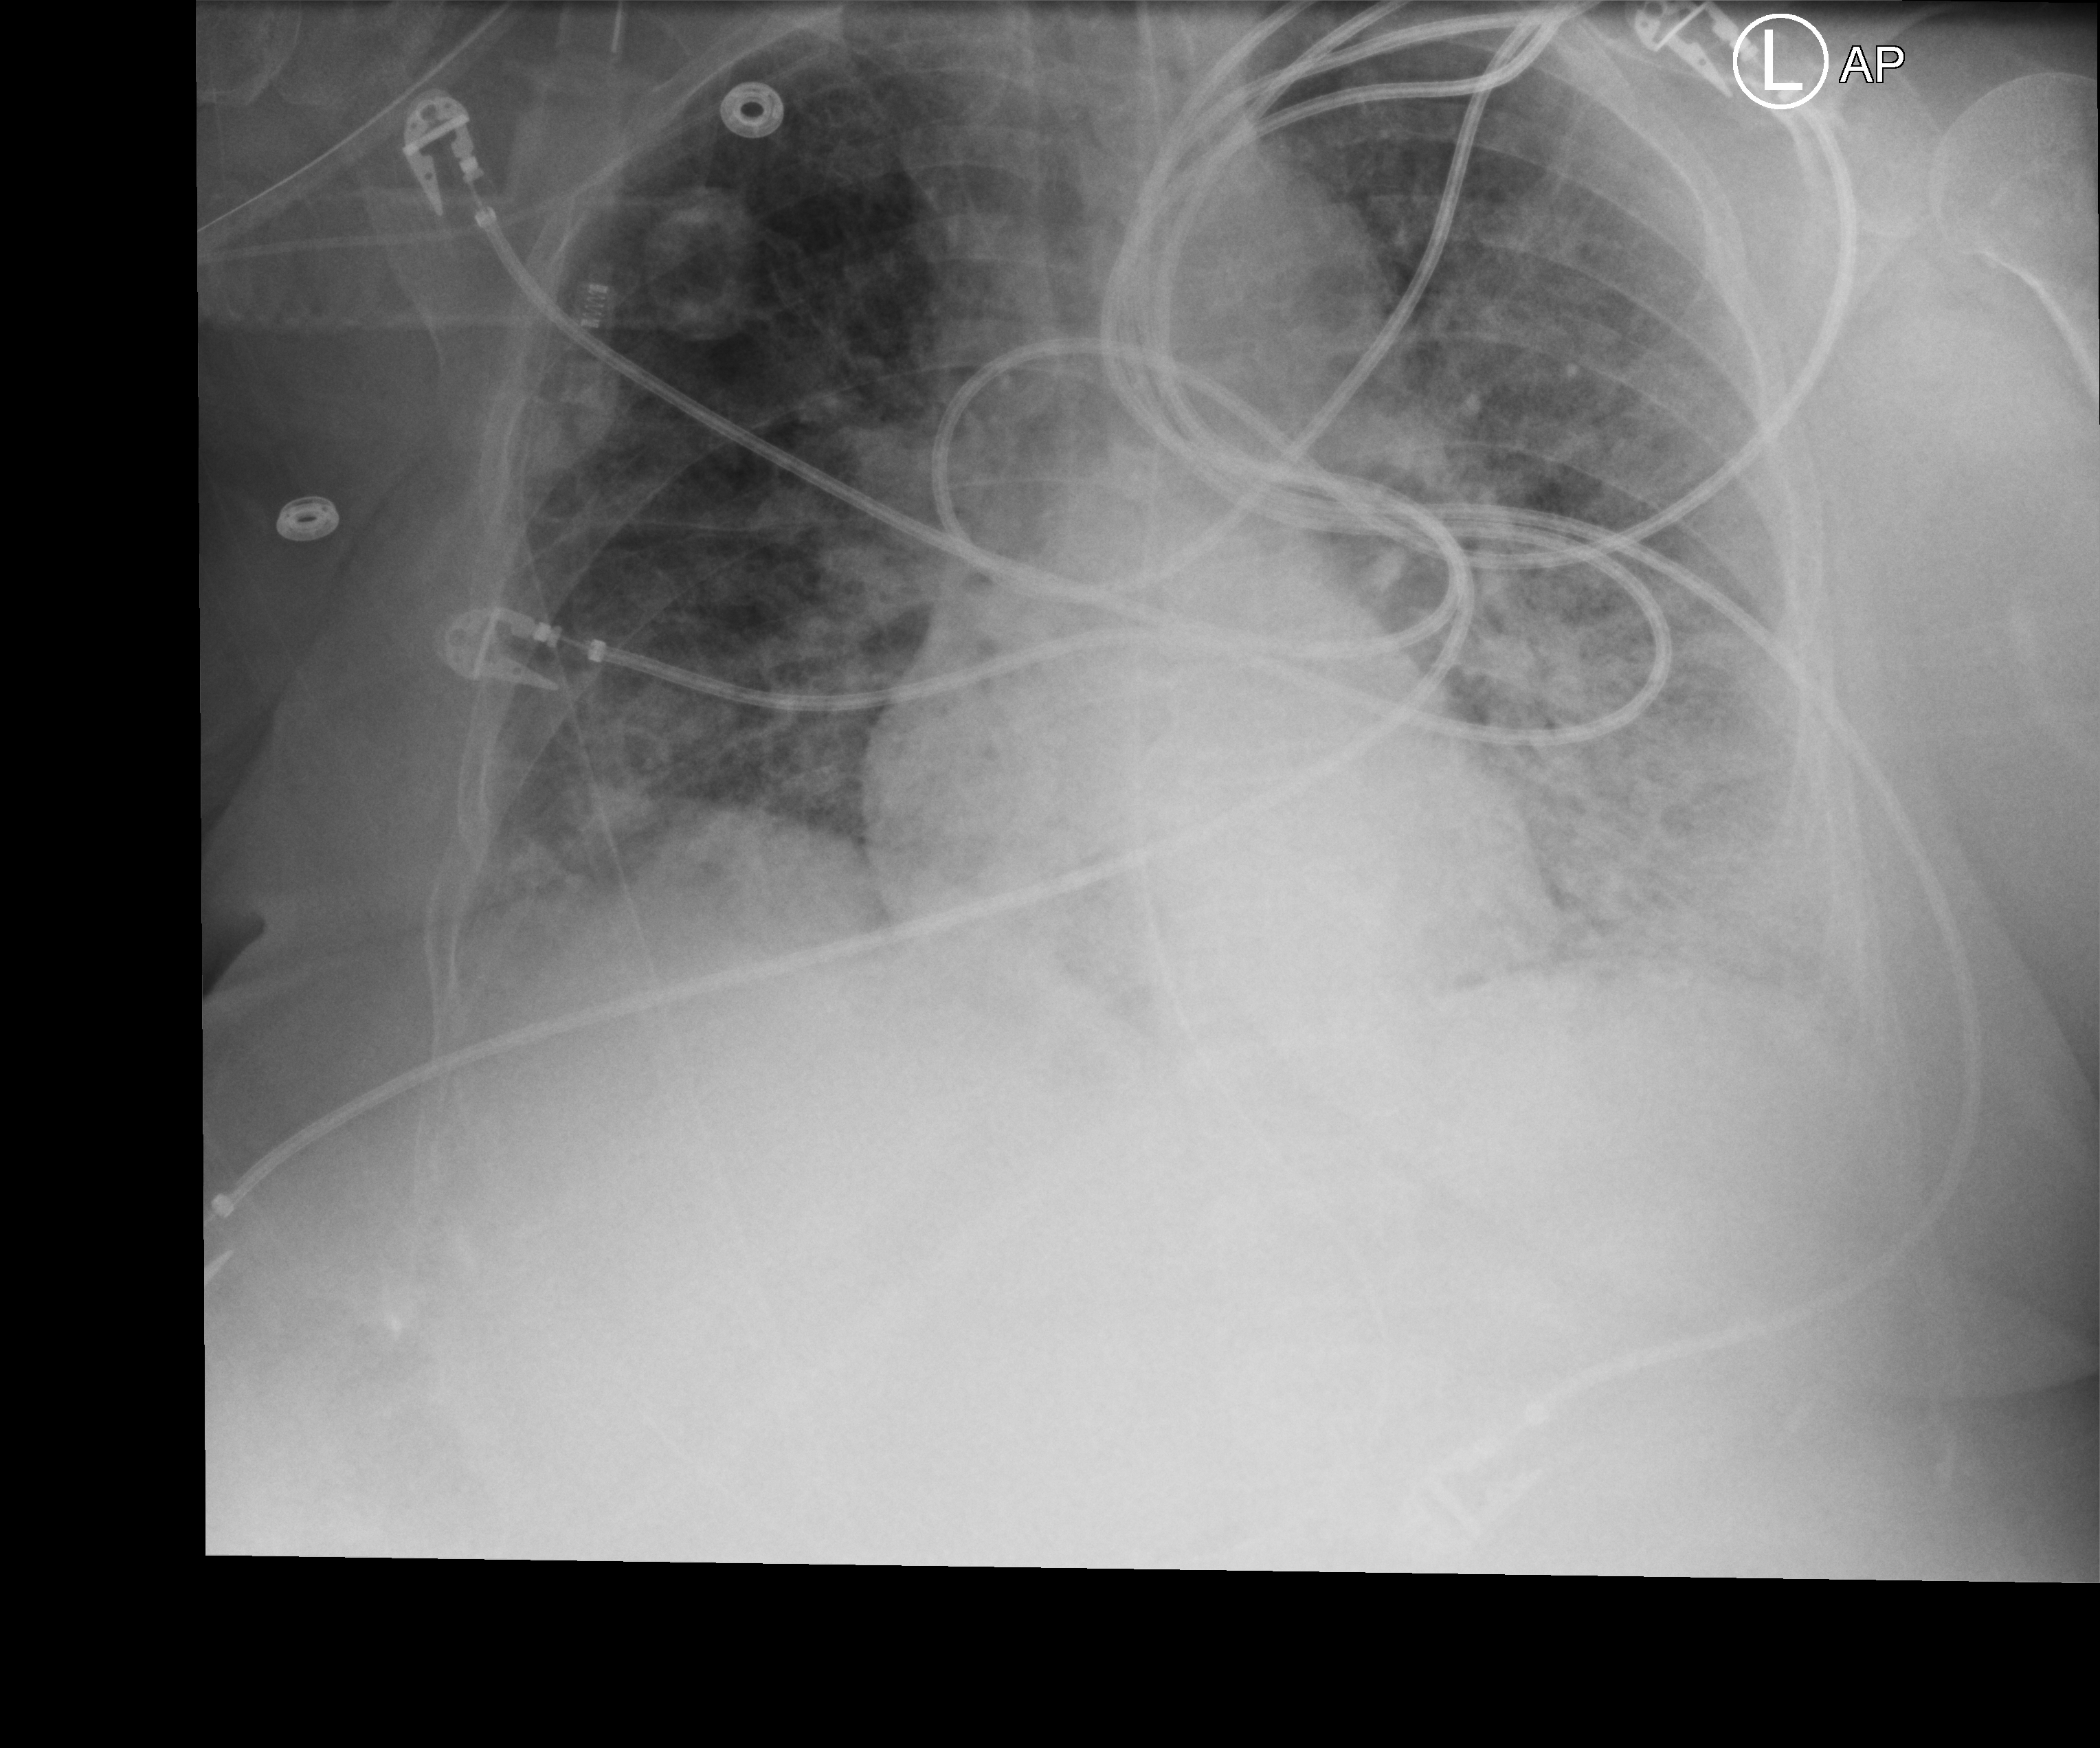
Portable chest radiograph; anteroposterior (AP) projection. Female patient hospitalised with COVID-19, age 60–74 years.
From the hospital-stay record, not from the radiograph (when in the stay this image was taken is not recorded): mechanically ventilated during this hospital stay: yes; diabetes (admission record): yes; smoking status (admission record): never.